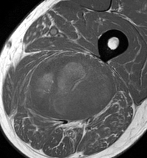
MRI of an extremity soft-tissue mass, one axial slice. MR volume resampled by the dataset authors to the PET/CT grid (not the native acquisition matrix). 3.27 mm slice thickness. 147 × 158 image matrix, field of view 144 × 154 mm. Male patient. From the clinical record (not read from this slice): histological type: undifferentiated pleomorphic liposarcoma; grade: high; site of the primary tumour: left thigh.
Outlined on this slice (expert contour drawn on MRI and transferred to this co-registered scan by the dataset authors):
- gross tumour volume including surrounding oedema: bounding box [x1, y1, x2, y2] px = [19, 56, 115, 128]
- gross tumour volume (mass): [28, 56, 115, 120]